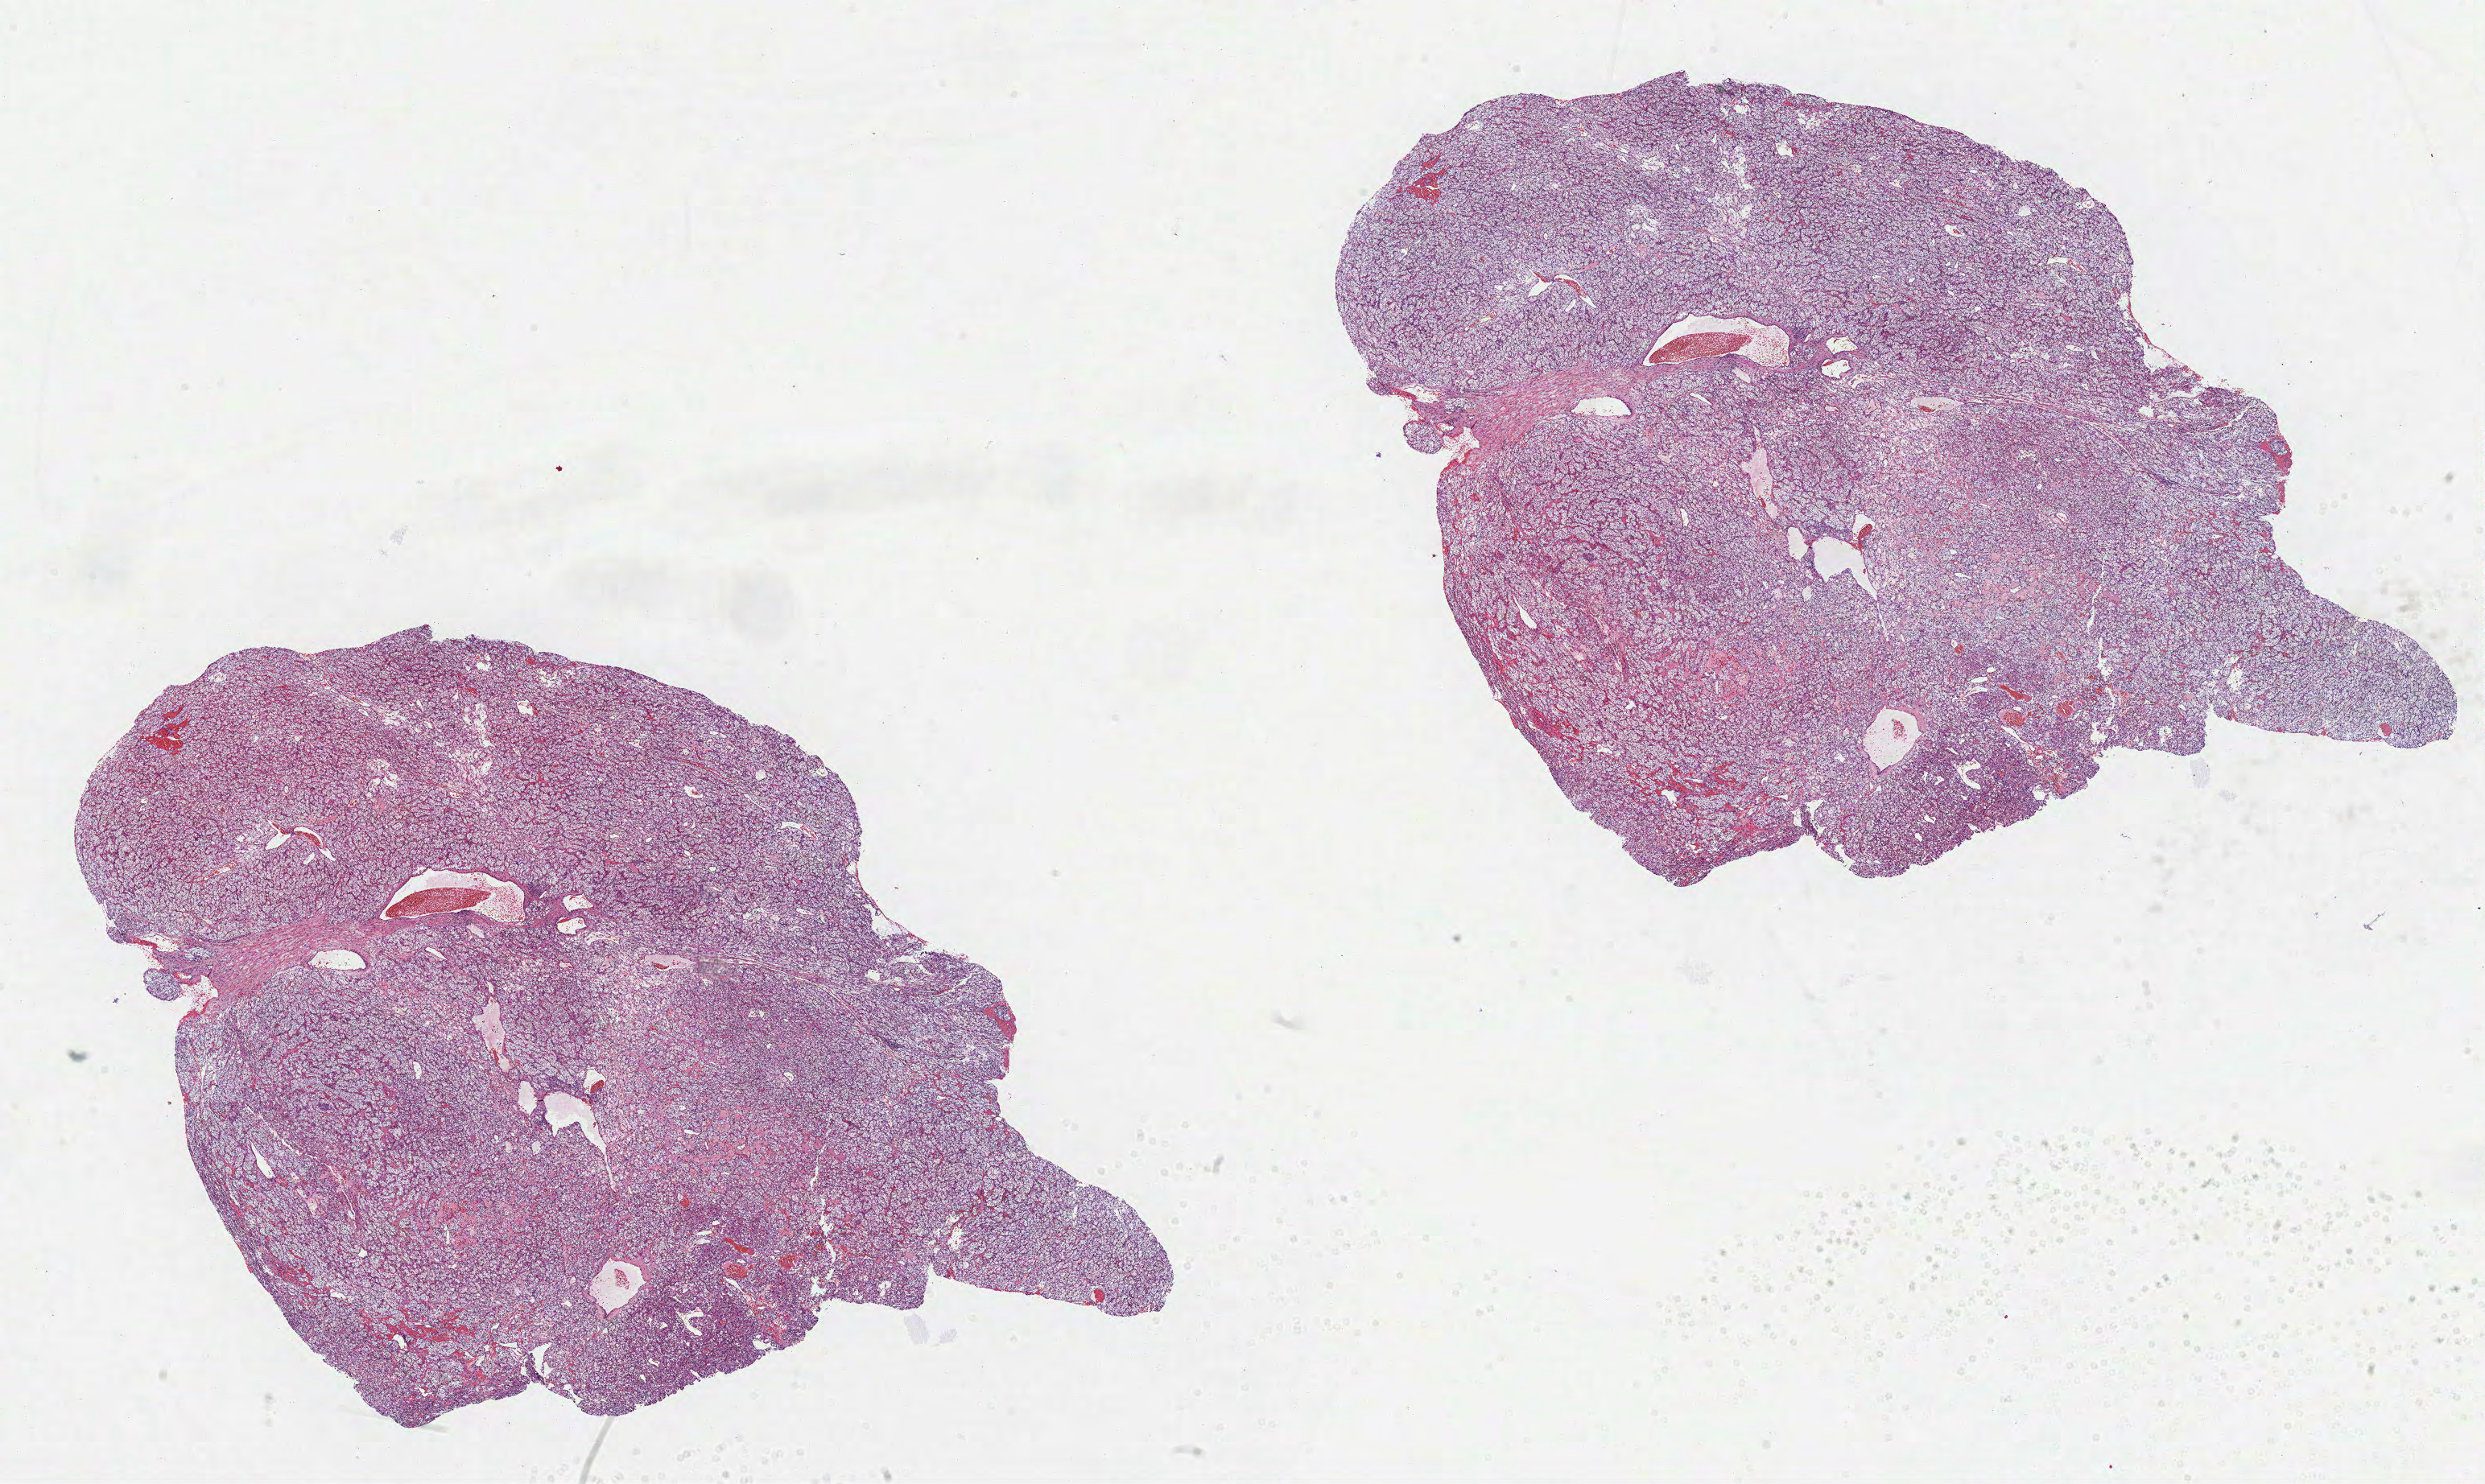
Digitized H&E tissue section (whole slide) — low-resolution overview of the scanned area, about 24.9 x 14.9 mm (from a 40x scan), formalin-fixed paraffin-embedded (FFPE) diagnostic section, kidney, primary tumour sample. Male, age 73 years at initial diagnosis. Histologic grade: G2 (moderately differentiated).
Laterality: left. Histologic diagnosis: Clear cell adenocarcinoma, NOS. AJCC pathologic stage: I.